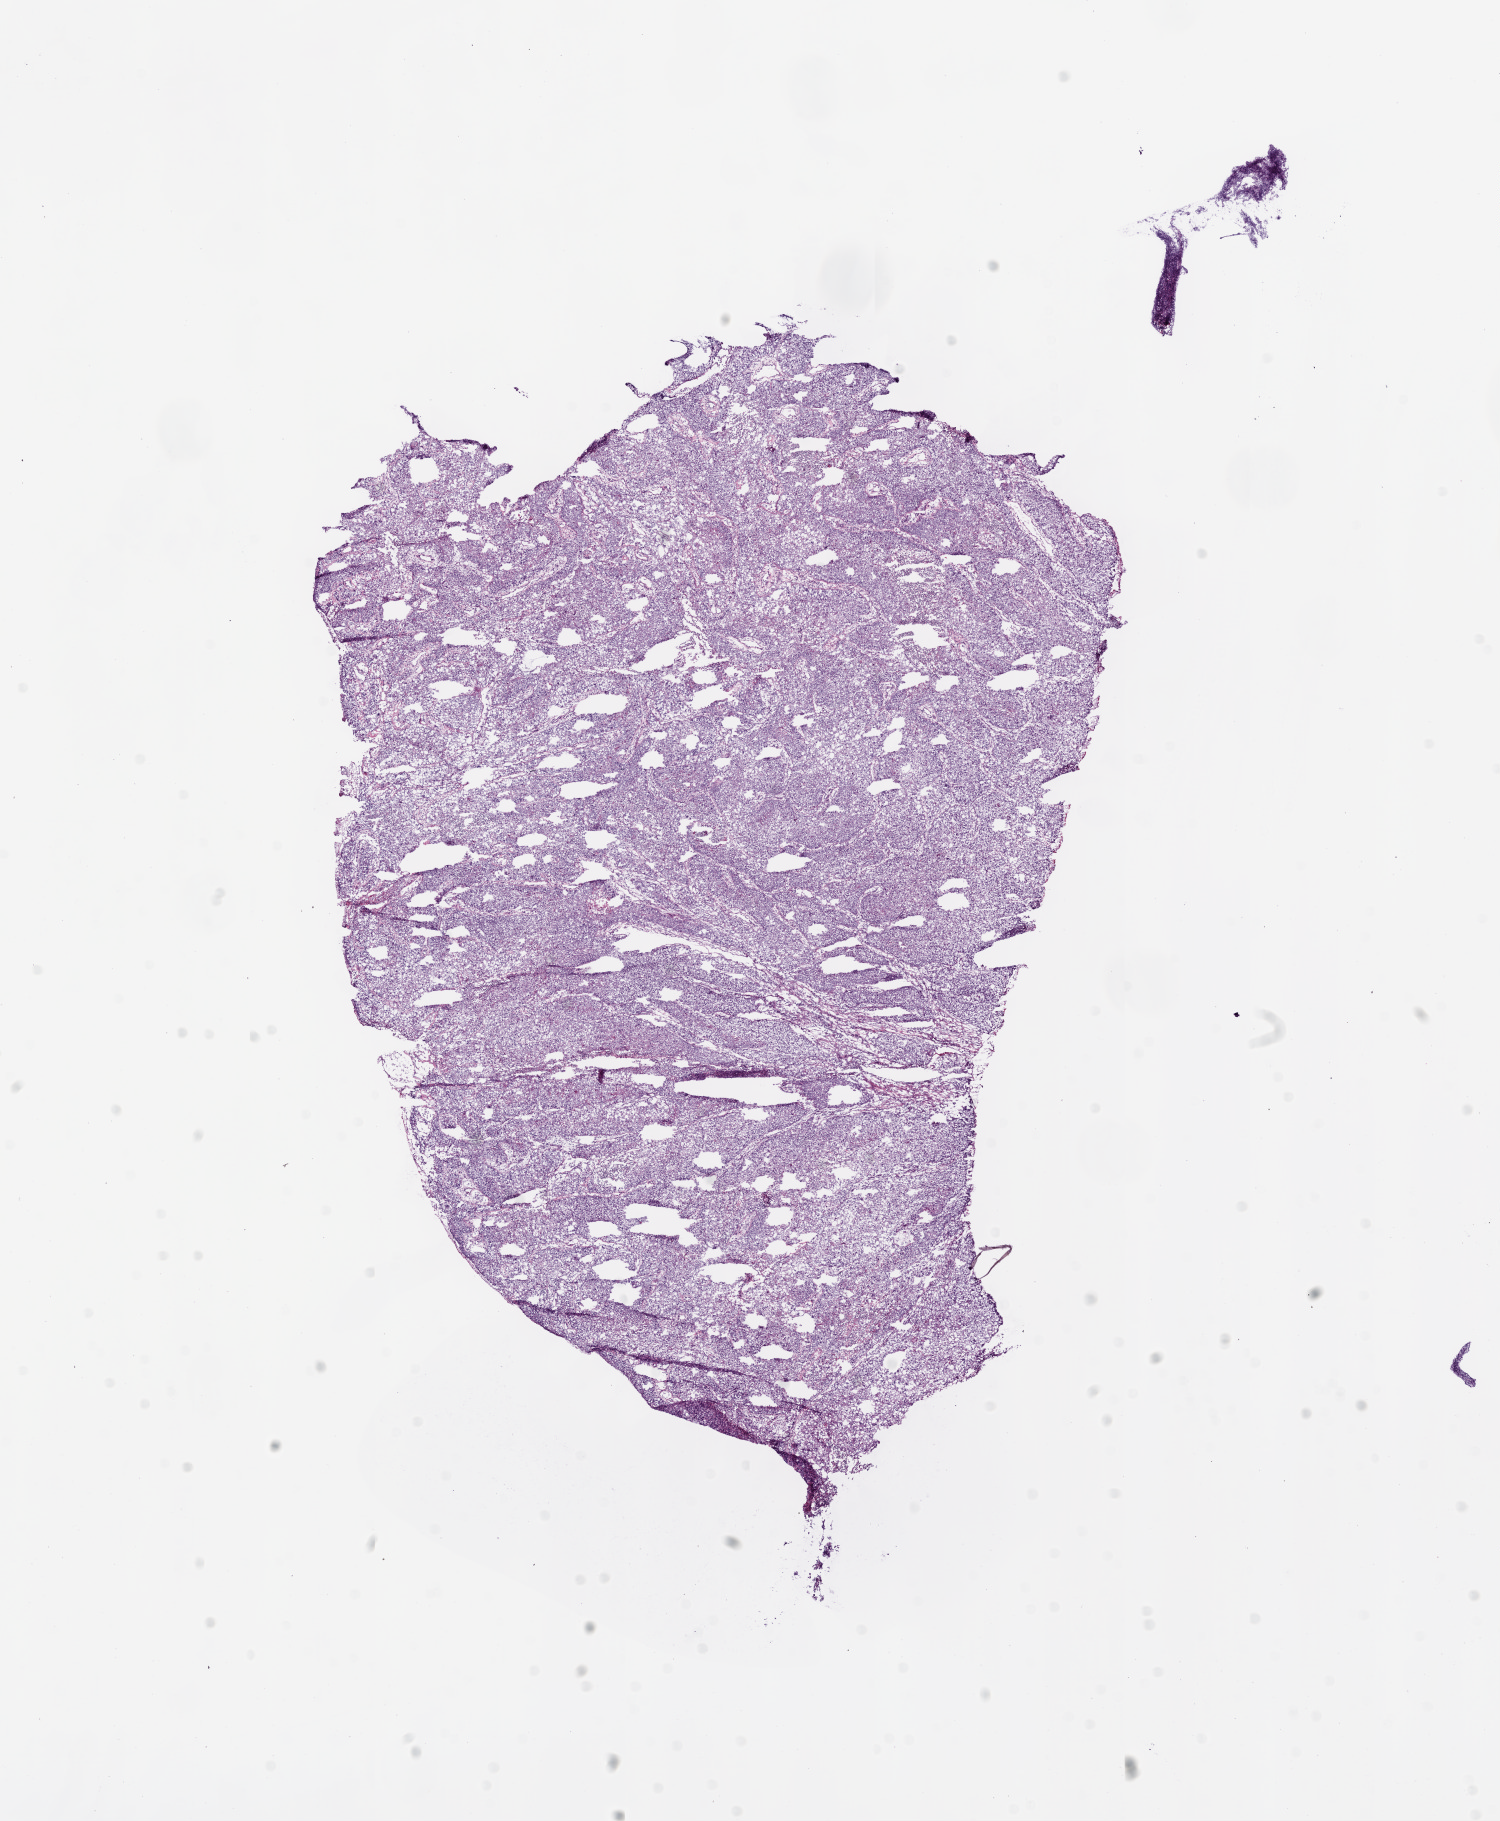
H&E whole-slide image, low-resolution overview of the scanned area, about 12.0 x 14.6 mm (from a 20x scan), frozen section, sample: primary tumour, lung. Male, age 57 years at initial diagnosis. Pathologist review of this section (percent, as recorded): tumour cells 90%, tumour nuclei 90%, normal cells 0%, stromal cells 5%, necrosis 5%.
- TNM: T2 N1 M0
- histologic diagnosis: Squamous cell carcinoma, NOS (lower lobe, lung)
- AJCC pathologic stage: IIB (6th edition)
- laterality: left